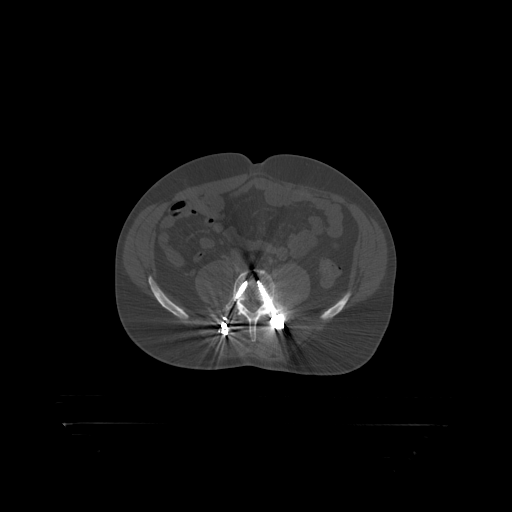
CT including the spine, one axial slice; position 210 of 399 along the scan axis; reconstruction kernel STANDARD; 120 kVp; bone window (W 1800 / L 400 HU); 1.25 mm slice thickness; 512 × 512 image matrix. Patient: male, 46 years. Case-level facts recorded for this patient, not image findings: primary cancer: skin.
Outlined on this slice (semi-automatically segmented with operator editing):
- L5 vertebra: box from (x=224, y=270) to (x=289, y=319) px